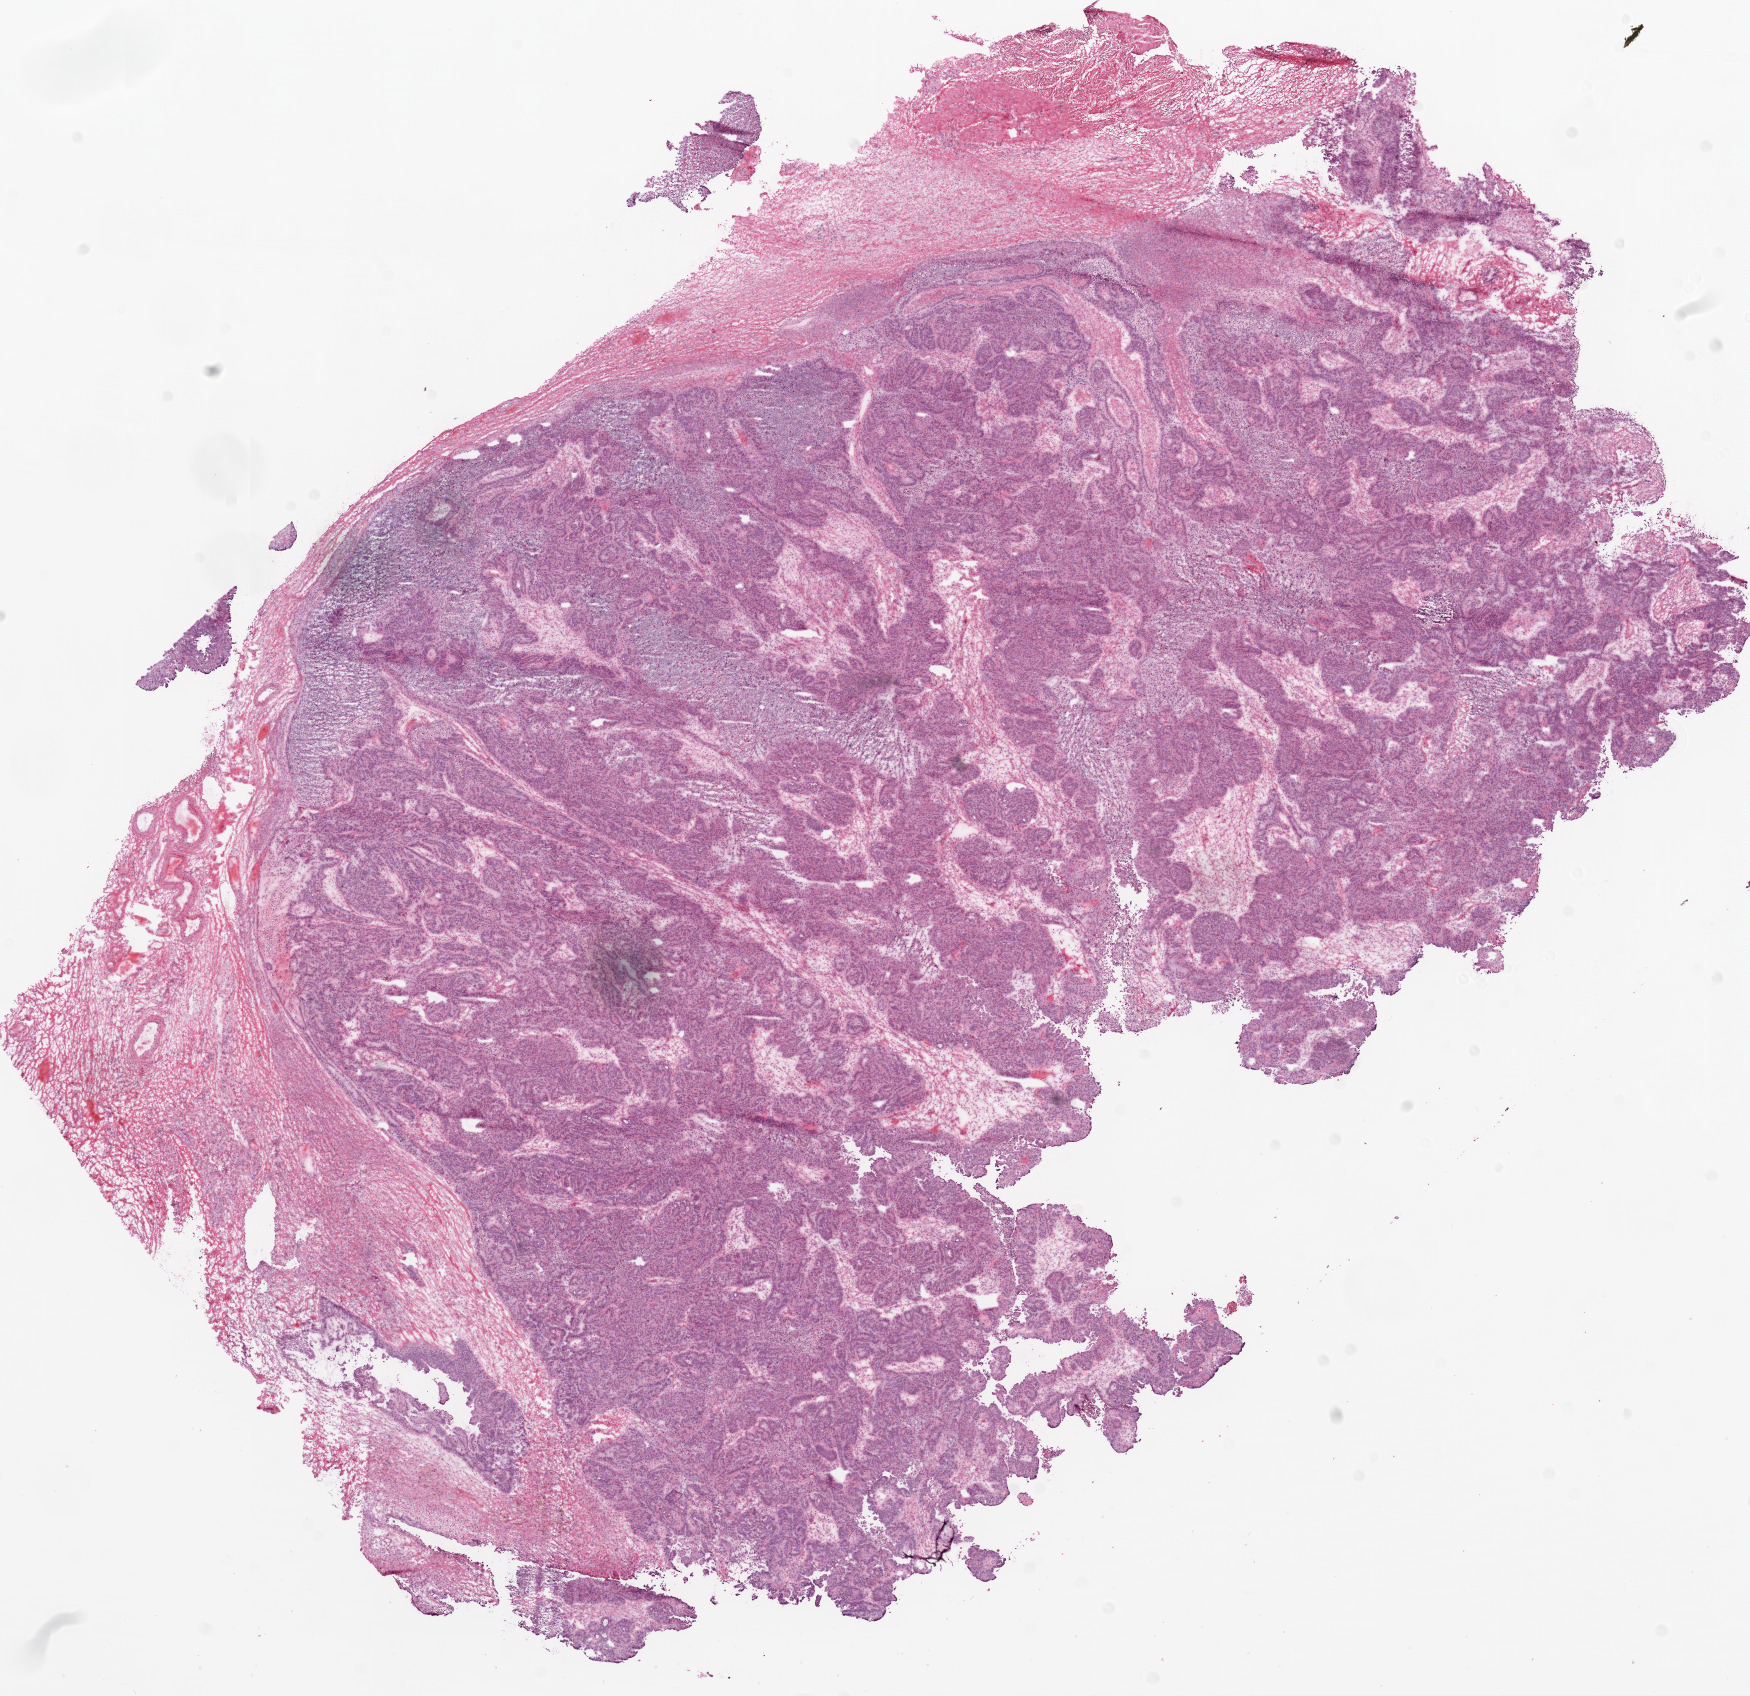
Hematoxylin and eosin (H&E) stained whole-slide image — a low-resolution overview of the entire scanned area, about 14.0 x 13.6 mm (from a 20x scan). Frozen section from the top of the tissue portion. Primary tumour sample from the ovary. Patient: female, age at initial diagnosis 73 years. Histologic grade: G3 (poorly differentiated). Composition of this section per pathologist review: tumour cells 89%, tumour nuclei 90%, normal cells 0%, stromal cells 10%, necrosis 1%.
FIGO stage: IIIC. Histologic diagnosis: Serous cystadenocarcinoma, NOS. Laterality: bilateral.